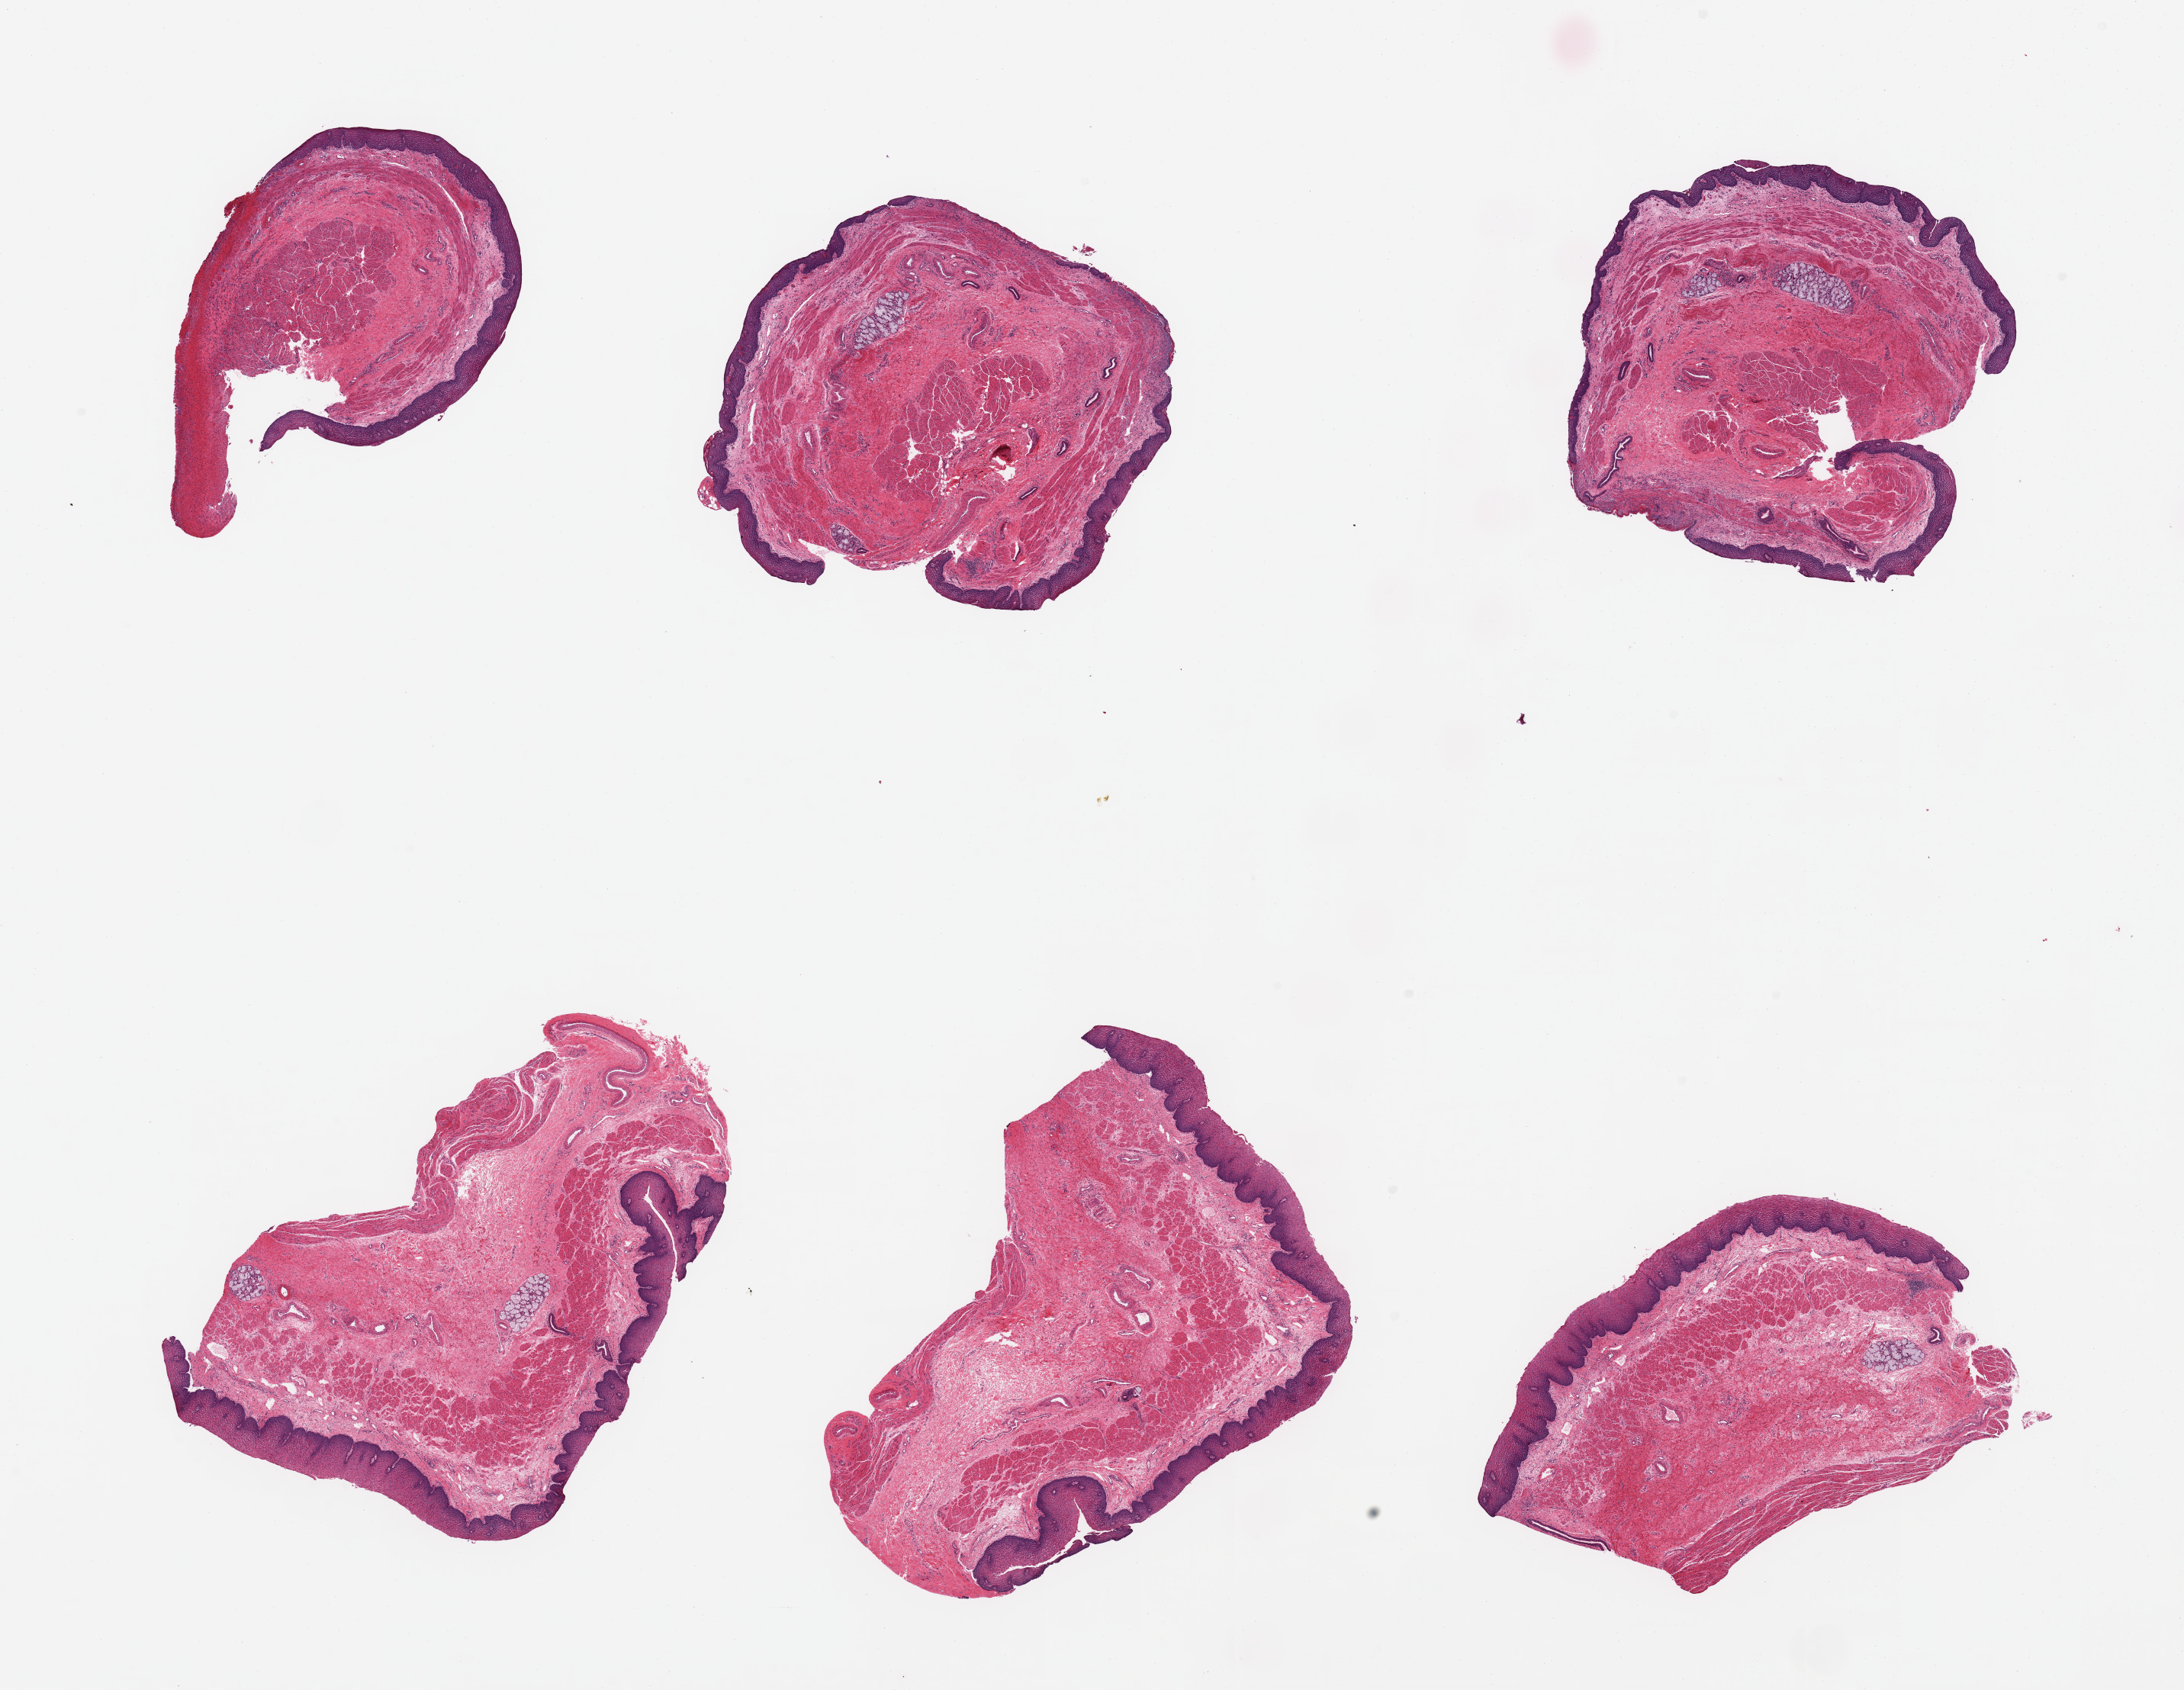
Hematoxylin and eosin (H&E) whole-slide image, low-resolution overview of the scanned area, about 22.6 x 17.5 mm, PAXgene-fixed paraffin-embedded (PFPE) section, target tissue: esophageal mucous membrane, donor tissue sample. Donor: male.
Pathologist's review note for this sample: 6 pieces, squamous mucosa up to ~0.4mm, ~15% thickness; A few submucosal mucus glands.